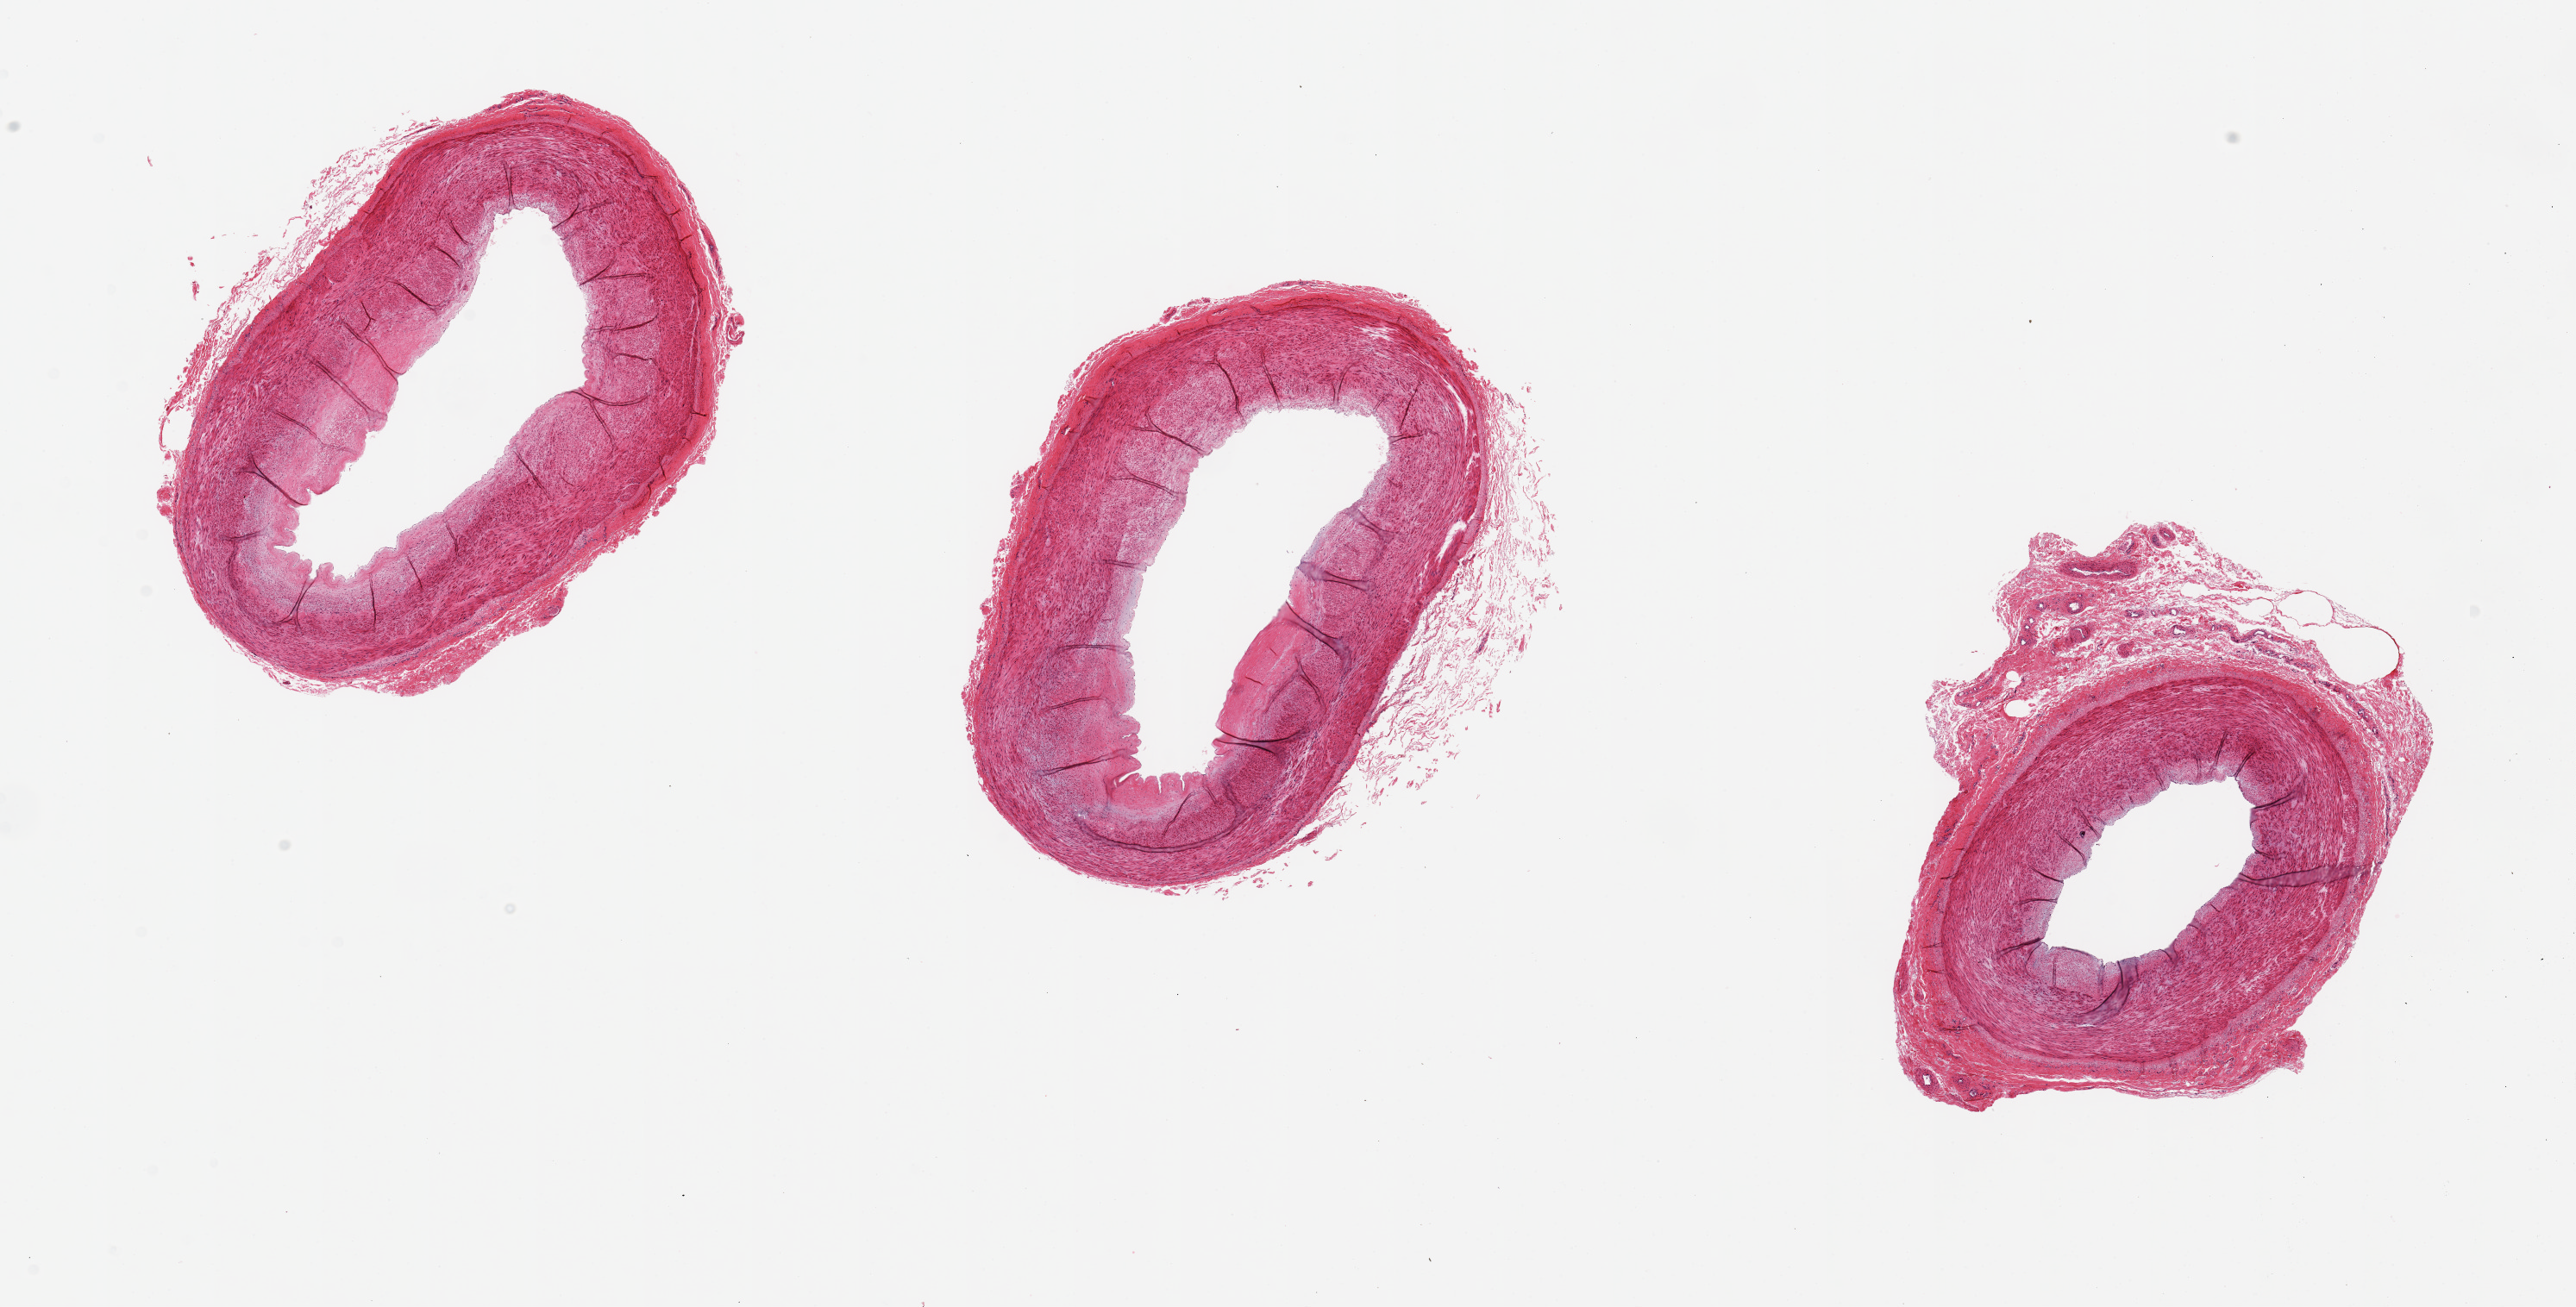
Digitized hematoxylin and eosin (H&E)-stained section, shown as a low-resolution overview of the whole scanned area (about 23.6 x 12.0 mm, slide scanned at 20x). PAXgene-fixed paraffin-embedded (PFPE) section. Sampled site (target tissue): tibial artery. Tissue donor sample.
- reviewer comment on this tissue sample: 3 pieces, up to 6x5mm; up to imm adherent fat, generally clean good specimens